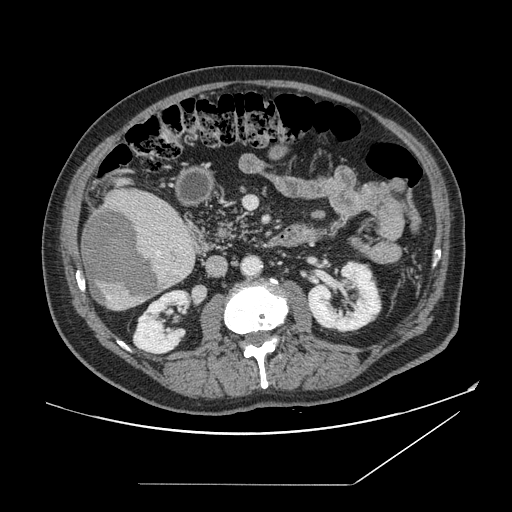
Contrast-enhanced abdominal CT, one axial slice. Slice 60 of 166 in the series (ordered by position). 120 kVp. Soft-tissue window (W 400 / L 40 HU). 2.5 mm slice thickness. 512 × 512 image matrix, field of view 416 × 416 mm. Male patient, age 80 years. Case-level facts recorded for this patient, not image findings: diagnosis: colorectal cancer liver metastases, imaged before liver resection; multiple liver metastases: no; largest metastasis: 2.2 cm; disease in both lobes: no.
Annotated regions visible in this slice (outlined manually by an expert reader):
- liver: box from (x=81, y=189) to (x=197, y=311) px
- planned liver remnant (the part of the liver to remain after resection): (x=133, y=191)–(x=168, y=208)
- liver metastasis: (x=84, y=207)–(x=164, y=304)